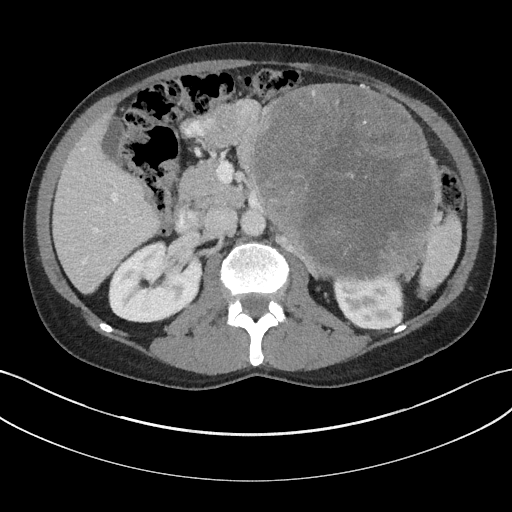
Contrast-enhanced abdominal CT, one axial slice. Slice 100 of 147 in the series (ordered by position). 100 kVp. Intravenous contrast given. Soft-tissue window (W 400 / L 40 HU). 3 mm slice thickness. 512 × 512 image matrix, field of view 384 × 384 mm. Male patient, age 58 years. From the clinical record (not read from this slice): diagnosis: adrenocortical carcinoma; tumour side: left adrenal; tumour size at pathology: 22 cm; Ki-67 index: 26 %.
Outlined on this slice (semi-automatically segmented with operator editing):
- mass: bounding box [x1, y1, x2, y2] px = [254, 85, 435, 277]